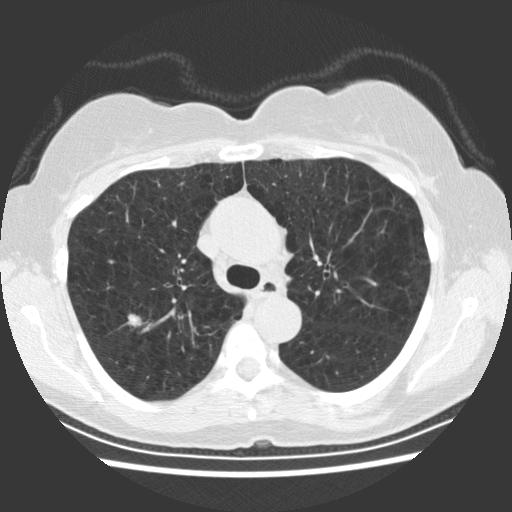
Low-dose screening chest CT, axial slice, baseline annual screen, lung window (W 1500 / L -600 HU), 2.5 mm slice thickness, standard (soft-tissue) reconstruction kernel (STANDARD), slice 70 of 234 in the series. Female, age 66 years at enrolment. Former smoker at enrolment.
Expert-annotated lung lesion, bounding box <111,300,153,339> (left, top, right, bottom; pixels). Screening reader's record for this exam (one nodule recorded; not confirmed to be the boxed lesion): non-calcified nodule or mass ≥4 mm, right upper lobe, 10 × 8 mm, smooth margins, soft tissue attenuation. Official screen result: positive, change unspecified: nodule(s) >= 4 mm or enlarging nodule(s), mass(es), or other non-specific abnormalities suspicious for lung cancer.